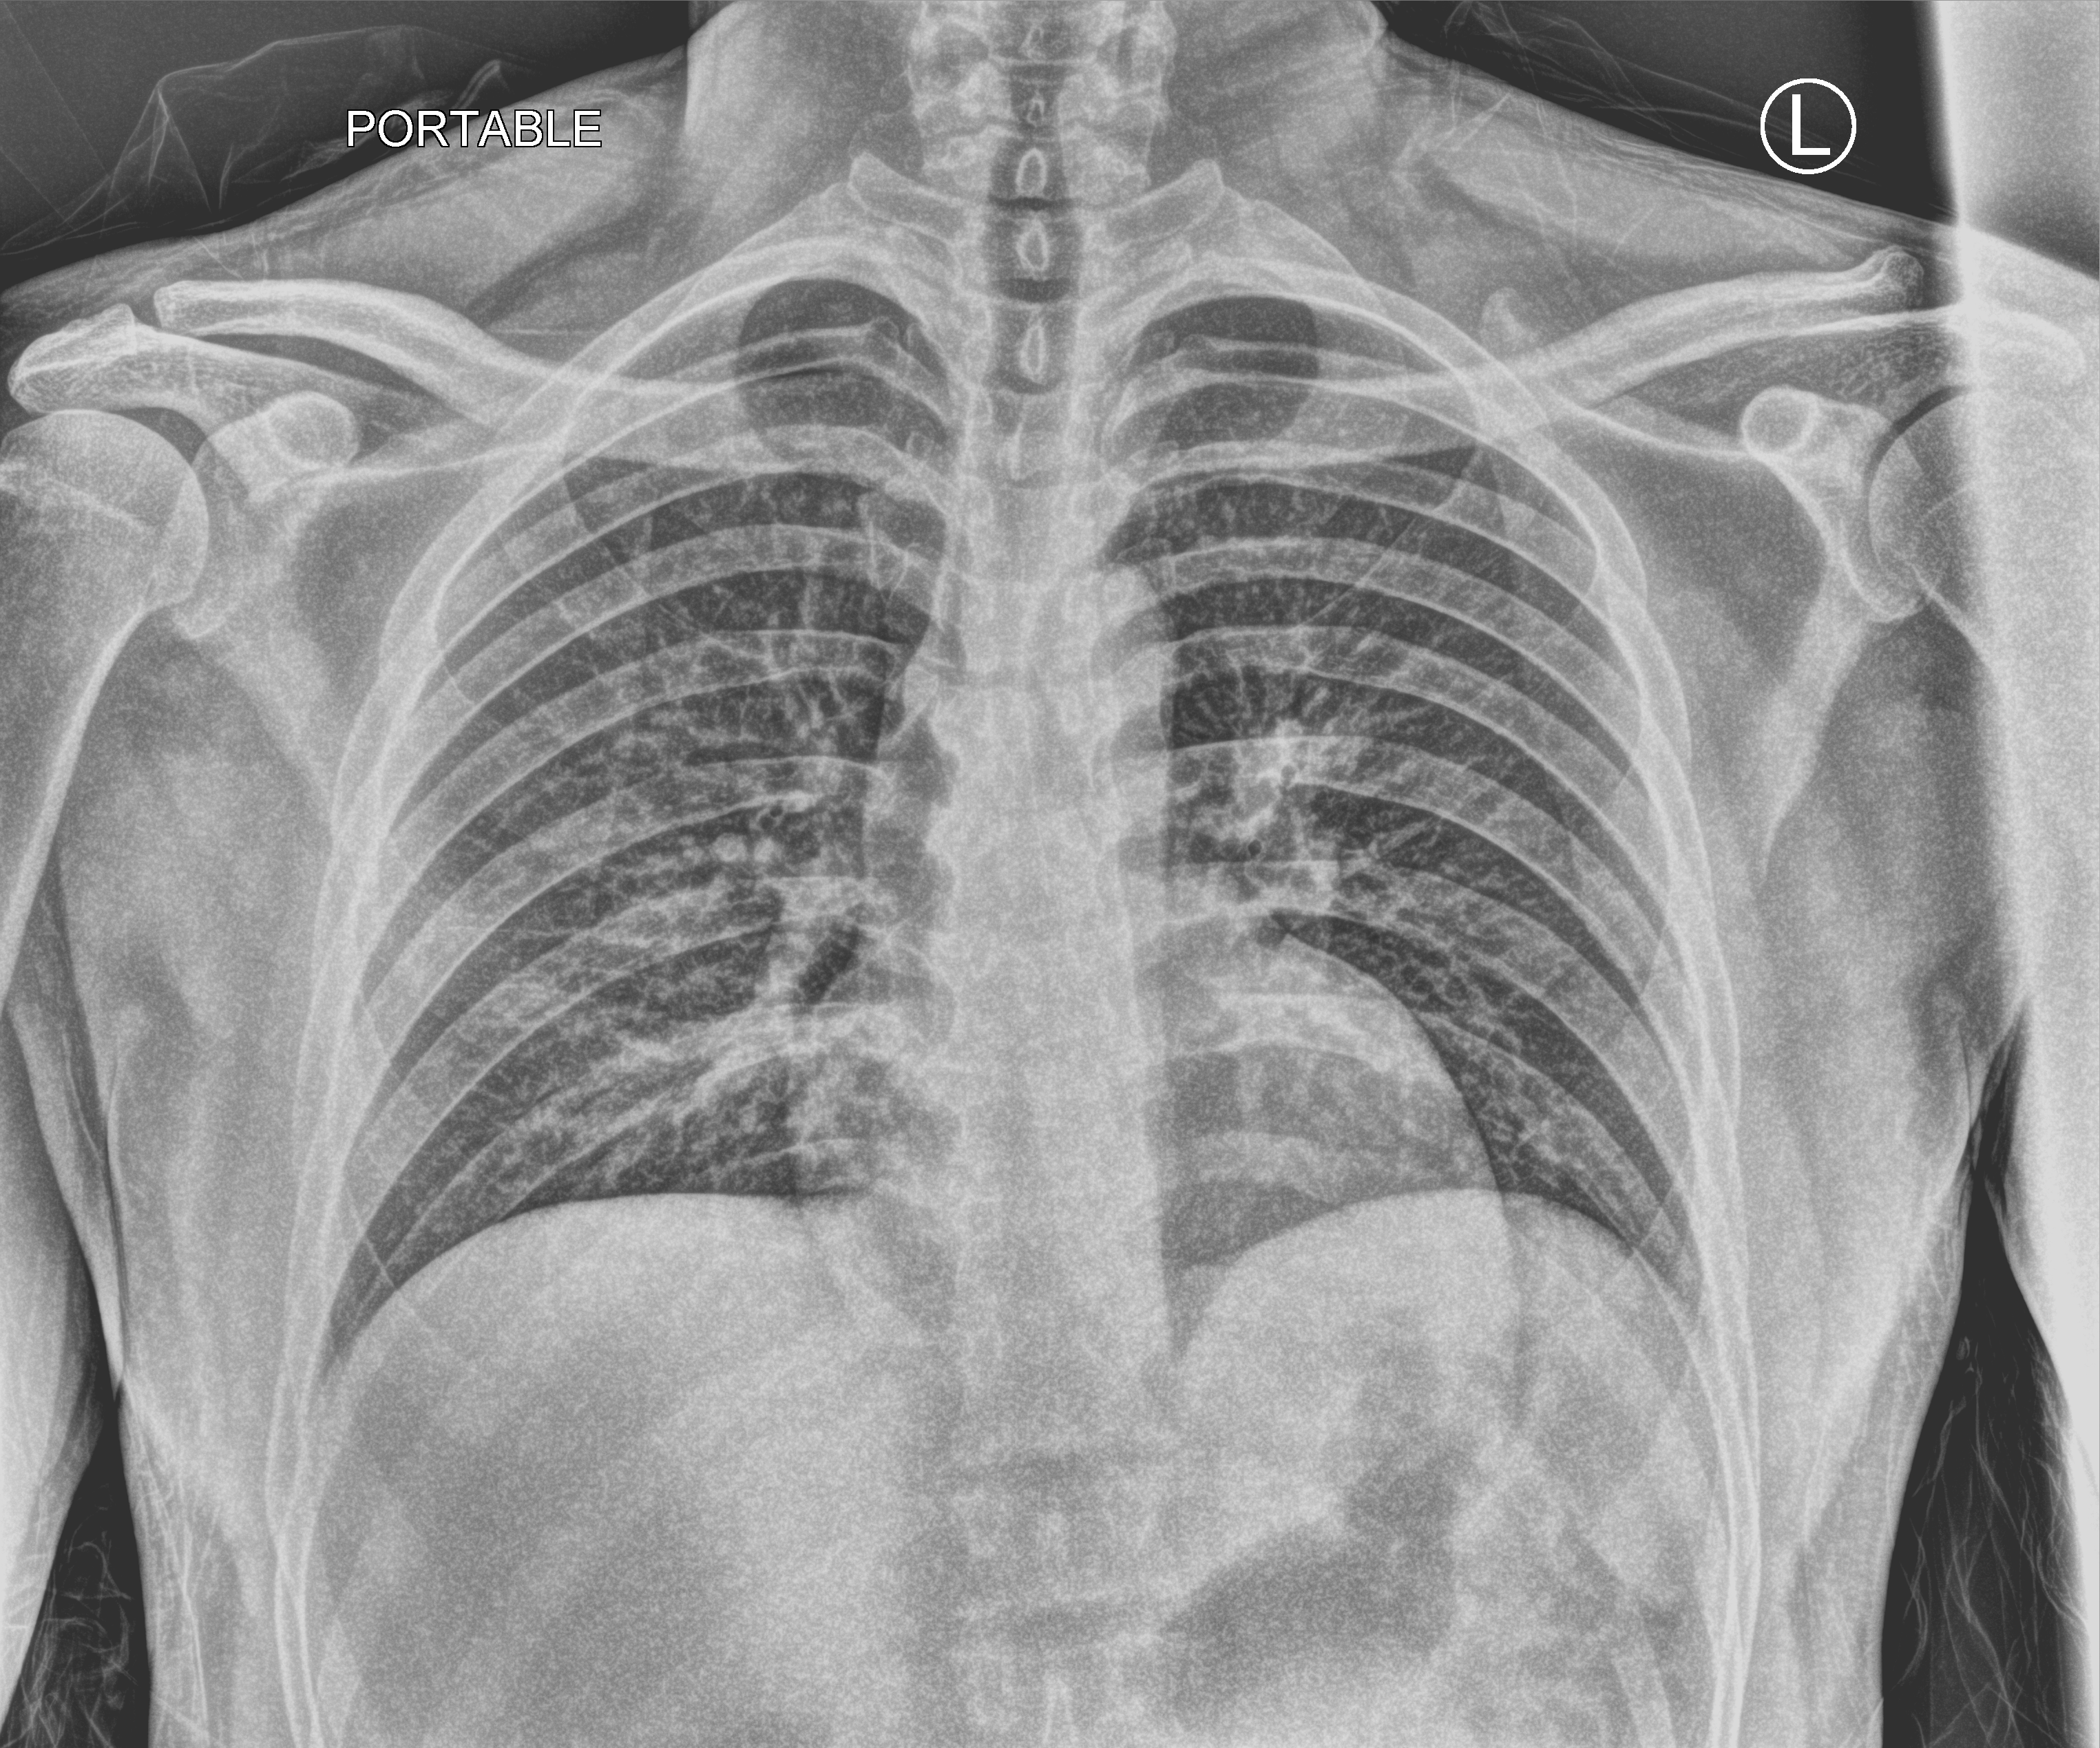
Bedside chest radiograph (computed radiography); anteroposterior (AP) projection. Patient hospitalised with COVID-19; male, aged 18–59 years.
Hospital-stay facts (about this admission, not read from this image; timing relative to this image not recorded):
- mechanically ventilated during this hospital stay: no